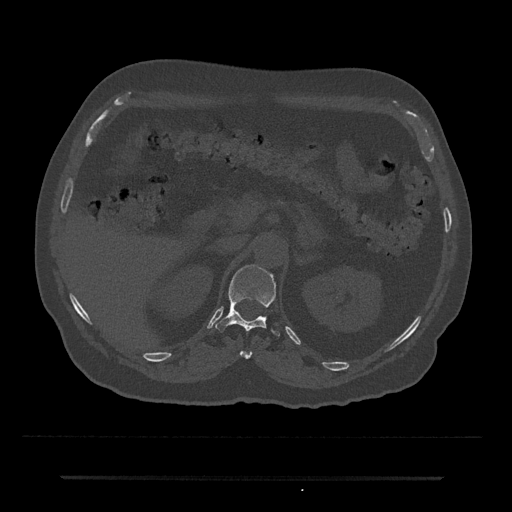
CT including the spine, one axial slice; slice 129 of 797 in the series (ordered by position); bone window (W 1800 / L 400 HU); 0.5 mm slice thickness; 512 × 512 image matrix, field of view 437 × 437 mm. Patient: male, 69 years. From the clinical record (not read from this slice): primary cancer: prostate.
Outlined on this slice (semi-automatically segmented with operator editing):
- T11 vertebra: box from (x=240, y=351) to (x=252, y=359) px
- T12 vertebra: (x=215, y=265)–(x=280, y=336)